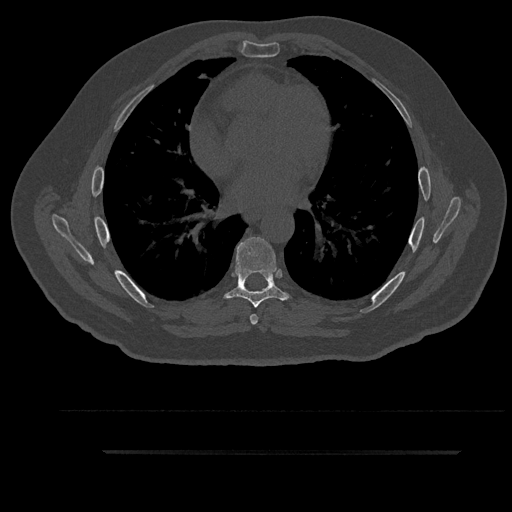
CT including the spine, one axial slice. Position 533 of 797 along the scan axis. Reconstruction kernel Br40s/3. Bone window (W 1800 / L 400 HU). 0.5 mm slice thickness. 512 × 512 image matrix, field of view 432 × 432 mm. Patient: male, 63 years. From the clinical record (not read from this slice): primary cancer: renal; vertebrae with lytic lesions (as recorded): T8.
Structures marked on this image (semi-automatically segmented with operator editing):
- T6 vertebra: bounding box <250,291,262,325> (left, top, right, bottom; pixels)
- T7 vertebra: <225,237,288,308>